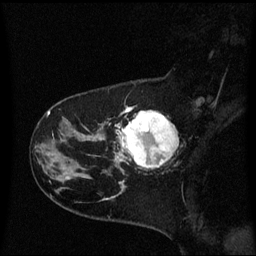
Breast MRI (dynamic contrast-enhanced), one sagittal slice; dynamic contrast-enhanced series, image 2 of 3 at this slice position (ordered by acquisition); 1.5 T; TE 4.2 ms, TR 8.4 ms; 2 mm slice thickness; 256 × 256 image matrix. Patient: female, 41 years. From the clinical record (not read from this slice): setting: breast cancer imaged before/during neoadjuvant chemotherapy; receptor status: triple-negative.
Annotated regions visible in this slice (semi-automatic segmentation, software-assisted and operator-edited):
- analysis volume of interest (the breast-tissue region the enhancement analysis was run in; not a lesion): box from (x=116, y=112) to (x=179, y=175) px
- tumour enhancement mask (voxels above the 70 % enhancement threshold inside the analysis volume of interest): (x=116, y=112)–(x=178, y=169)